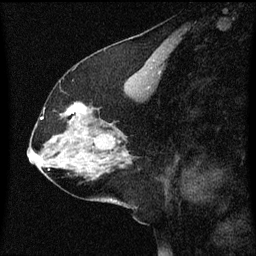
Breast MRI (dynamic contrast-enhanced), one sagittal slice. Slice 28 of 60 in the series (ordered by position). Dynamic contrast-enhanced series, image 2 of 3 at this slice position (ordered by acquisition). 1.5 T. TE 4.2 ms, TR 8 ms. 256 × 256 image matrix, field of view 200 × 200 mm. Female patient, age 58 years.
Outlined on this slice (semi-automatic segmentation, software-assisted and operator-edited):
- analysis volume of interest (the breast-tissue region the enhancement analysis was run in; not a lesion): box from (x=56, y=102) to (x=95, y=137) px
- tumour enhancement mask (voxels above the 70 % enhancement threshold inside the analysis volume of interest): (x=66, y=104)–(x=87, y=117)